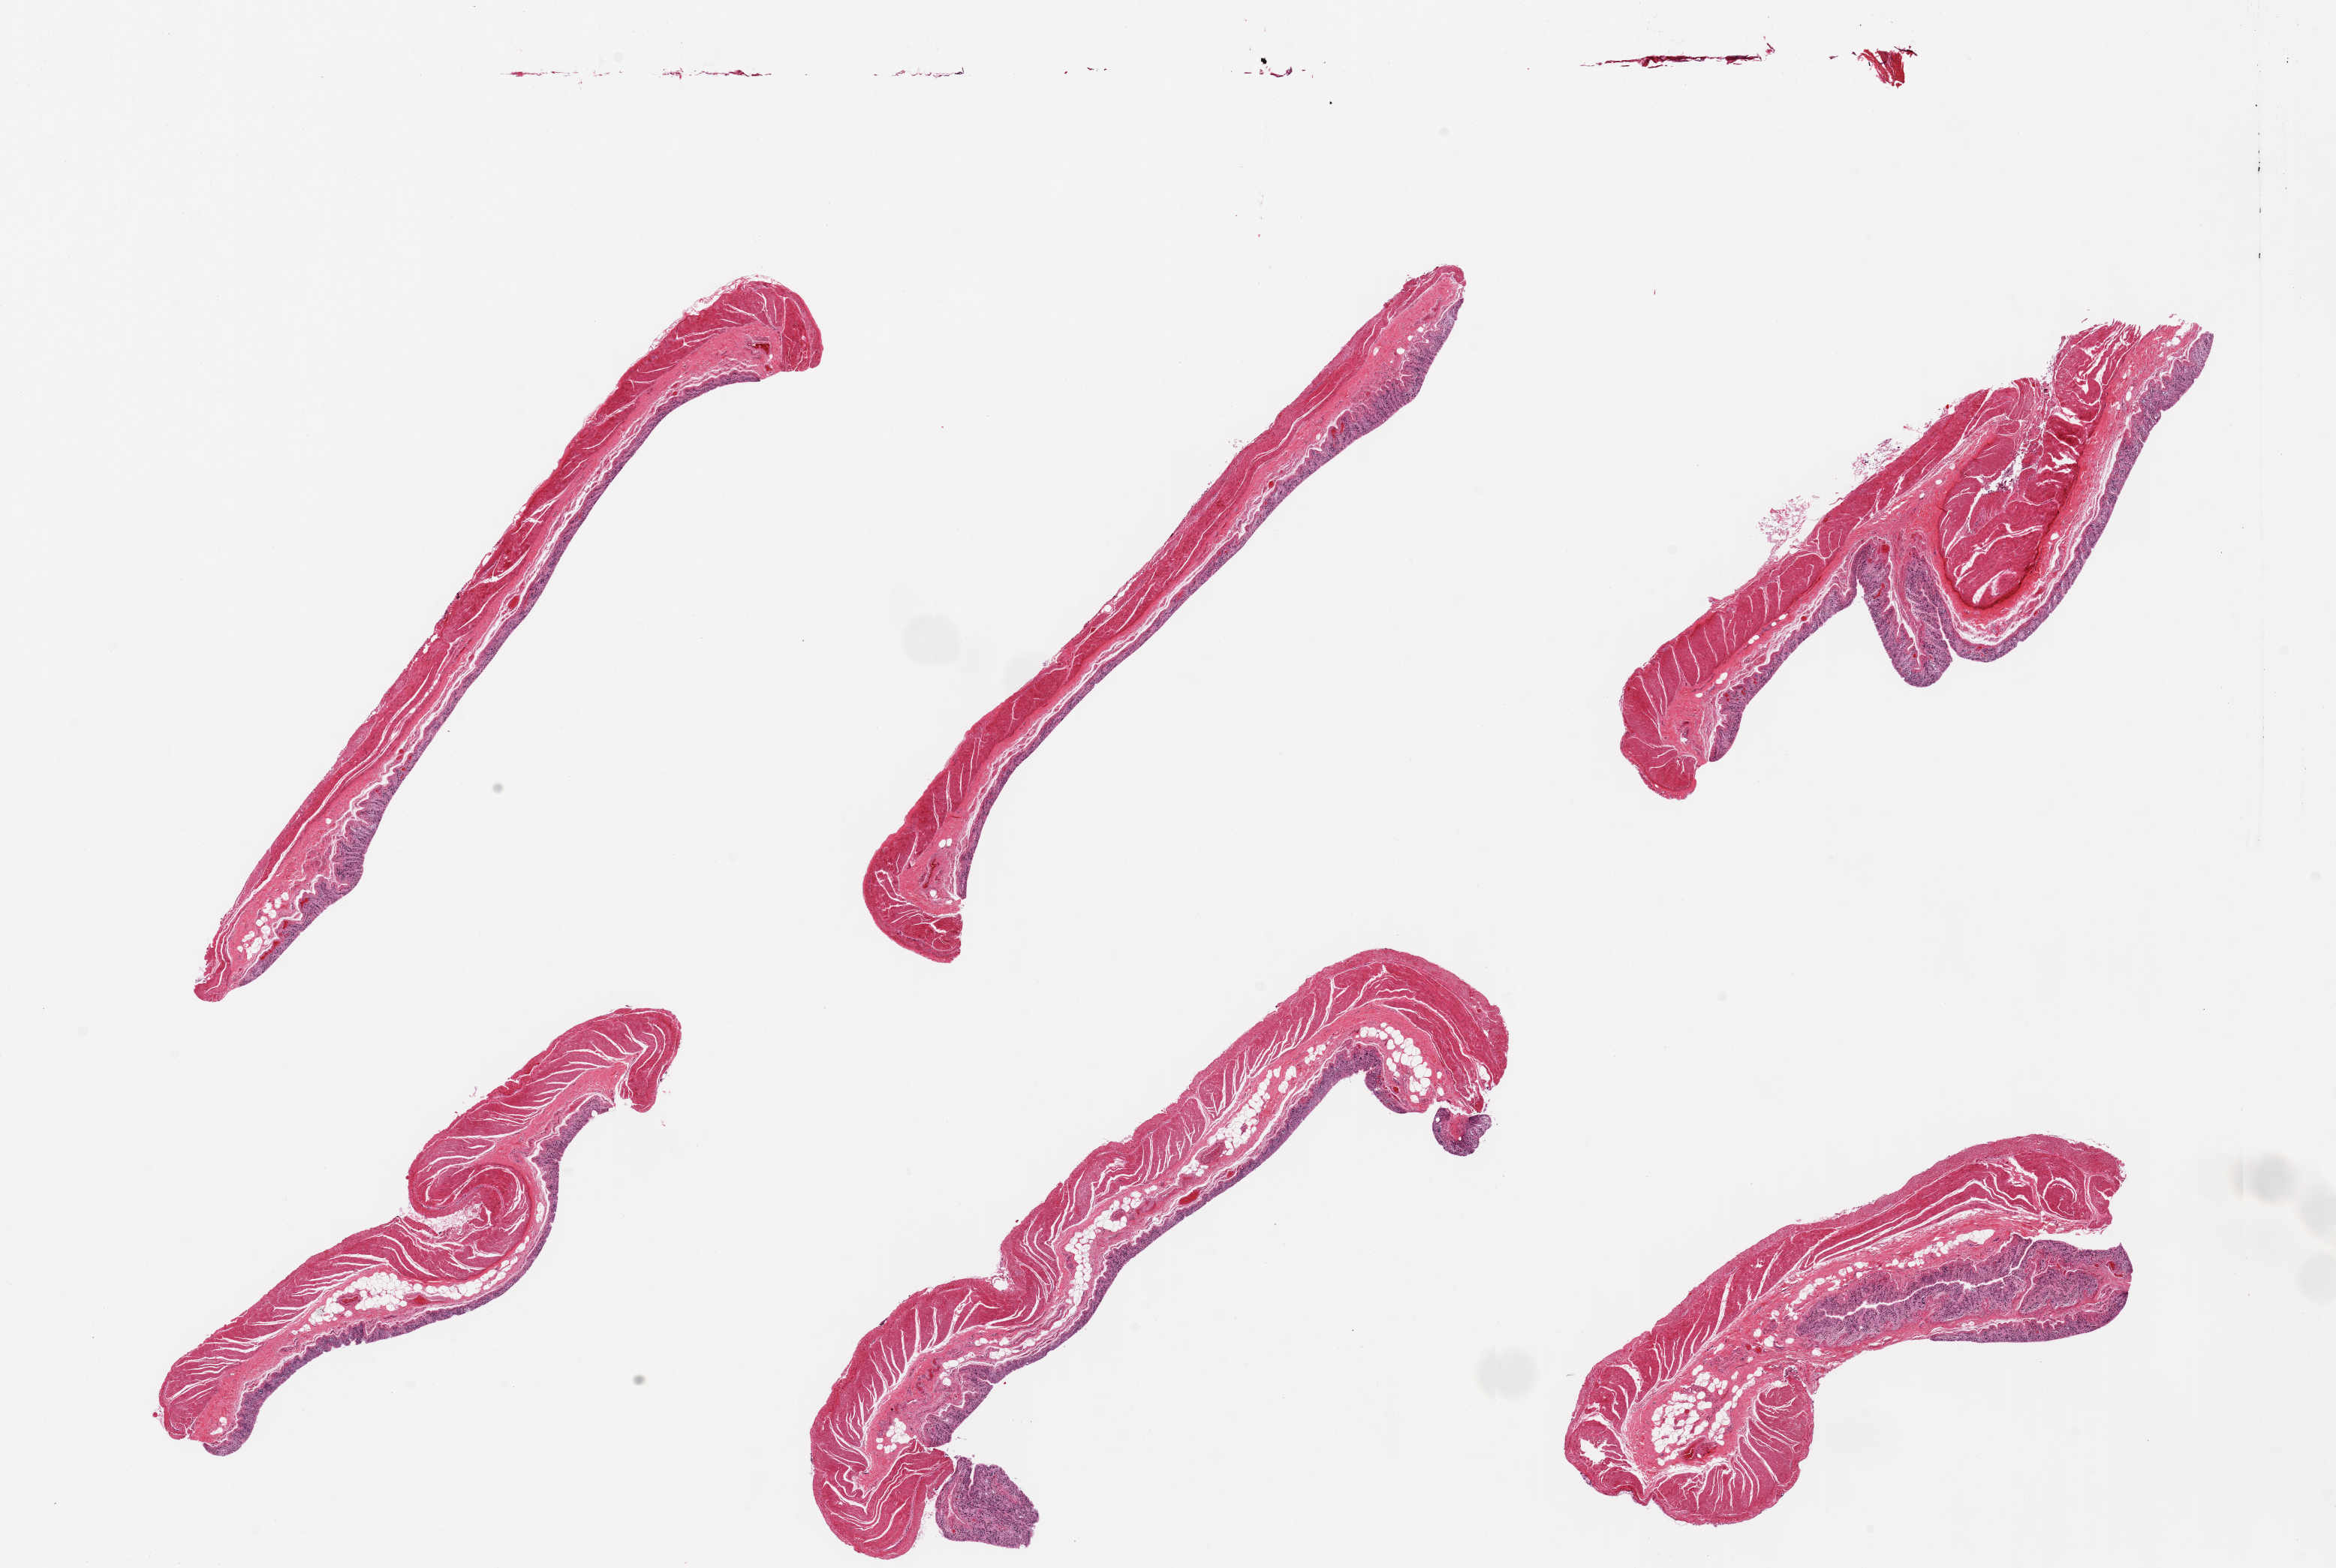
Hematoxylin and eosin (H&E) whole-slide image — shown as a low-resolution overview of the whole scanned area (about 24.6 x 16.5 mm, from a 20x scan), PAXgene-fixed, paraffin-embedded tissue, target tissue: transverse colon, donor tissue sample.
Reviewer comment on this tissue sample: 6 pieces, mucosa autolyzed (3), muscularis (1).